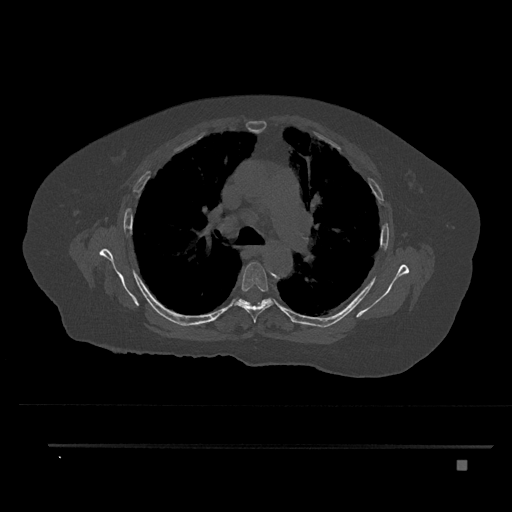
CT including the spine, one axial slice. Slice 559 of 797 in the series (ordered by position). 120 kVp. Bone window (W 1800 / L 400 HU). 0.5 mm slice thickness. 512 × 512 image matrix, field of view 437 × 437 mm. Female patient, age 76 years. From the clinical record (not read from this slice): primary cancer: lung; vertebrae with lytic lesions (as recorded): T11, L3.
Structures marked on this image (semi-automatic segmentation, software-assisted and operator-edited):
- T5 vertebra: box from (x=234, y=262) to (x=275, y=323) px
- T6 vertebra: (x=235, y=298)–(x=273, y=307)